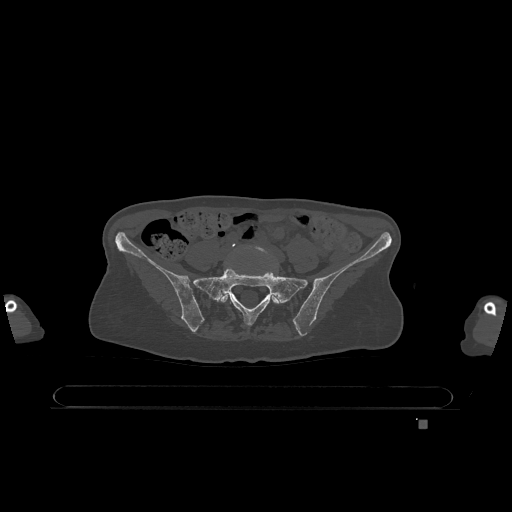
CT including the spine, one axial slice; slice 204 of 1317 in the series (ordered by position); bone window (W 1800 / L 400 HU); 0.5 mm slice thickness; 512 × 512 image matrix, field of view 500 × 500 mm. Patient: female, 74 years. Case-level facts recorded for this patient, not image findings: primary cancer: lung; vertebrae with lytic lesions (as recorded): T1, T4, T5, T6, L4, L5.
Structures marked on this image (semi-automatic segmentation, software-assisted and operator-edited):
- L5 vertebra: bounding box <219,245,280,304> (left, top, right, bottom; pixels)